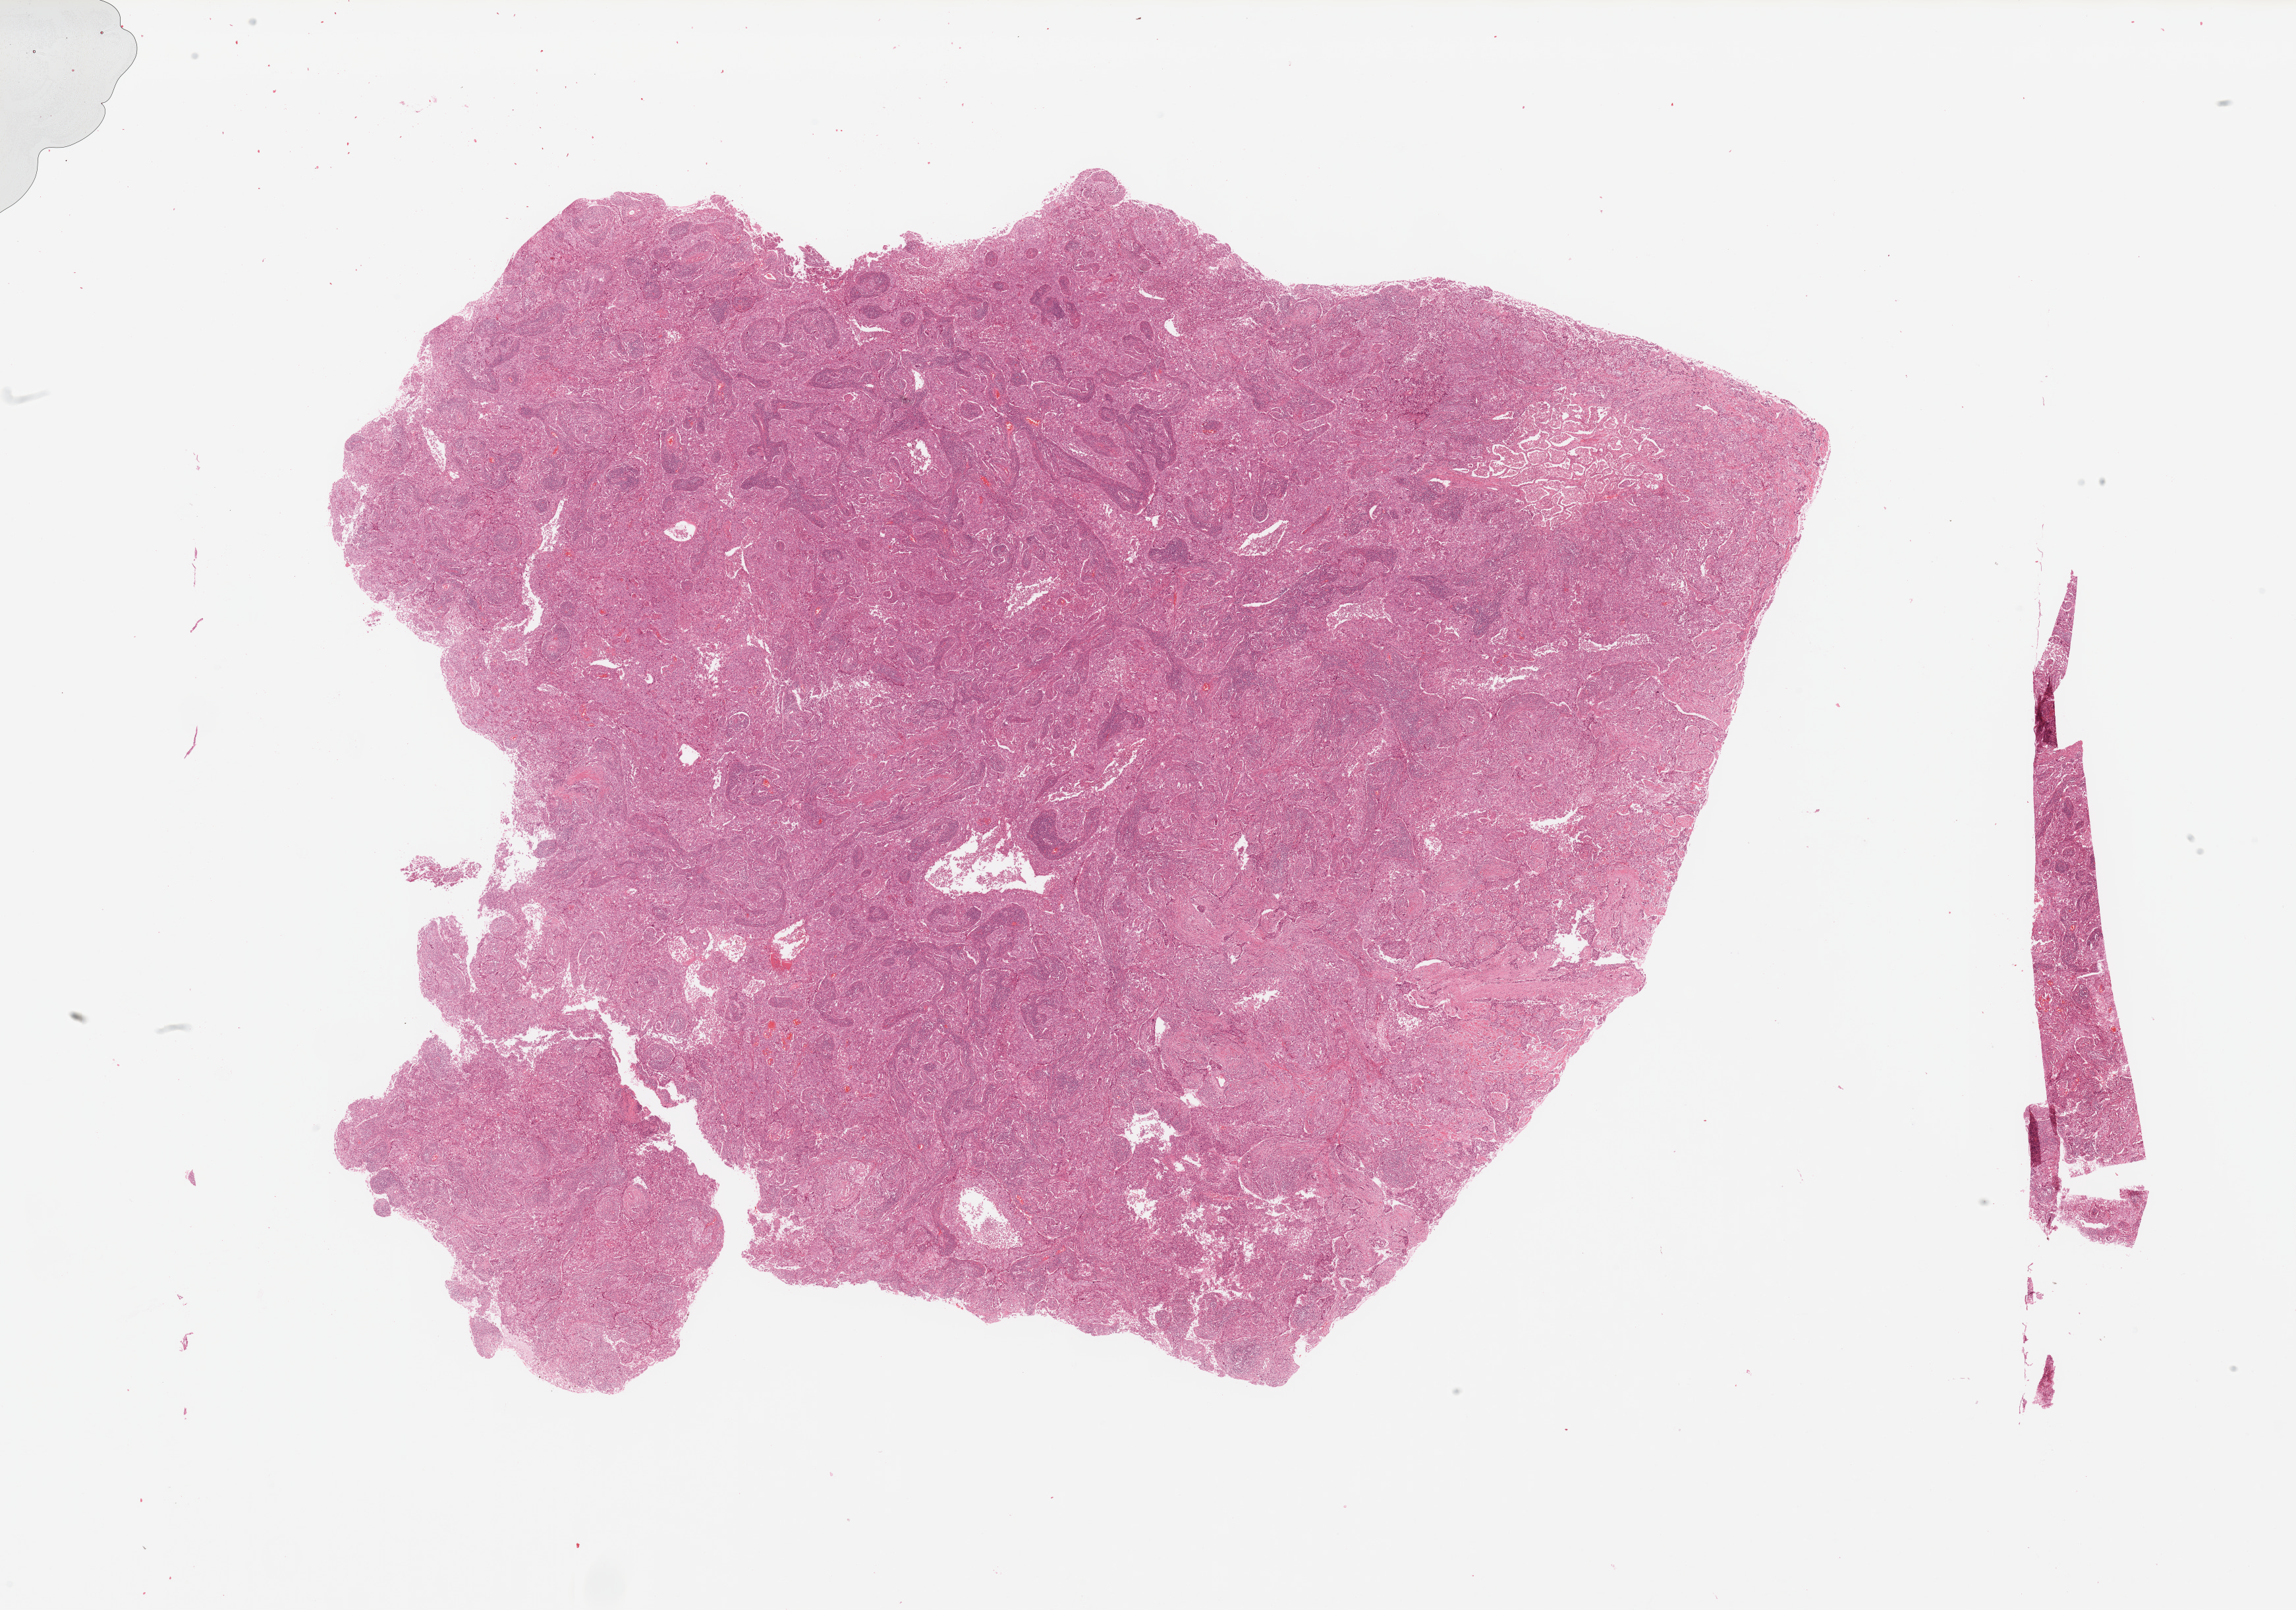
Whole-slide histology image, H&E-stained — a low-resolution overview of the entire scanned area, about 27.6 x 19.3 mm, tumour tissue sample, lung. Male, 60 y/o. Histologic grade: G3 (poorly differentiated).
AJCC pathologic stage: IIB. Histologic diagnosis: Adenocarcinoma, NOS.